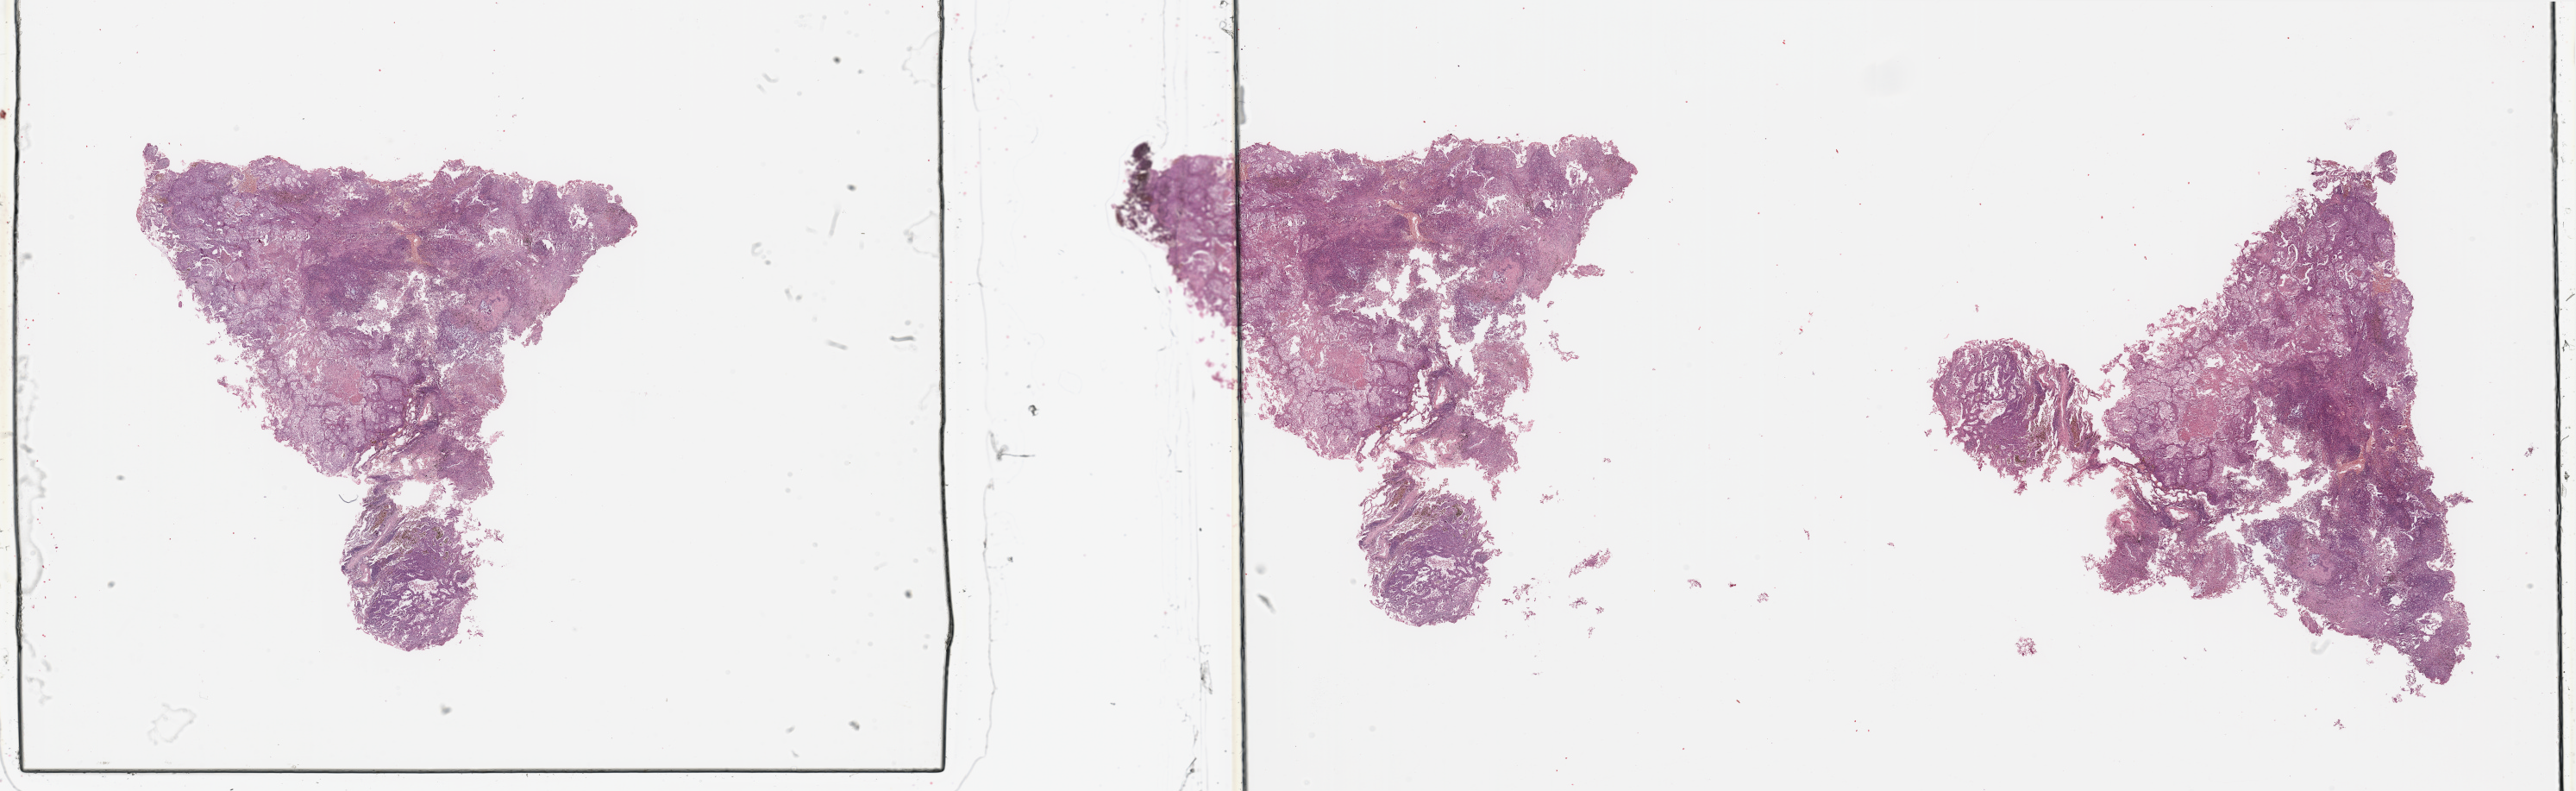
Digitized H&E tissue section (whole slide) — shown as a low-resolution overview of the whole scanned area (about 47.3 x 14.5 mm, slide scanned at 20x), lung, tumour tissue. 51-year-old male patient. Histologic grade: G3 (poorly differentiated).
• AJCC pathologic stage: IB
• primary tumour site (as recorded): right lower lobe
• histologic diagnosis: Adenocarcinoma, NOS